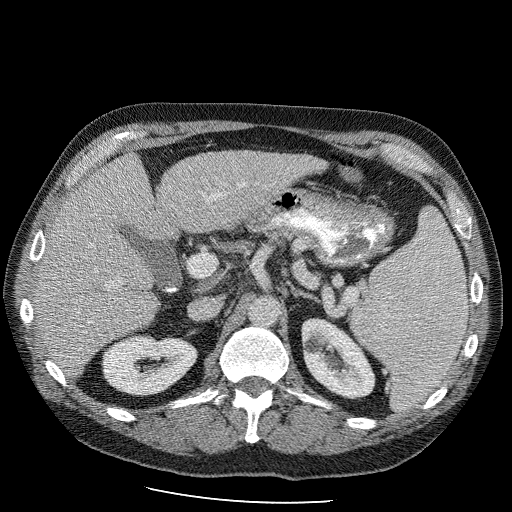
Contrast-enhanced abdominal CT (liver protocol), one axial slice. Position 52 of 98 along the scan axis. 120 kVp. Soft-tissue window (W 400 / L 40 HU). 2.5 mm slice thickness. 512 × 512 image matrix. From the clinical record (not read from this slice): diagnosis: hepatocellular carcinoma (patient treated with transarterial chemoembolisation; whether this scan precedes or follows treatment is not stated here); TNM stage (as recorded): Stage-II.
Structures marked on this image (semi-automatic segmentation, software-assisted and operator-edited):
- liver parenchyma outside the tumour (the mass and vessels are separate outlines, so this box may not span the whole liver): bounding box (x1, y1, x2, y2) in pixels: (30, 150, 327, 380)
- liver vessels: (80, 196, 256, 296)